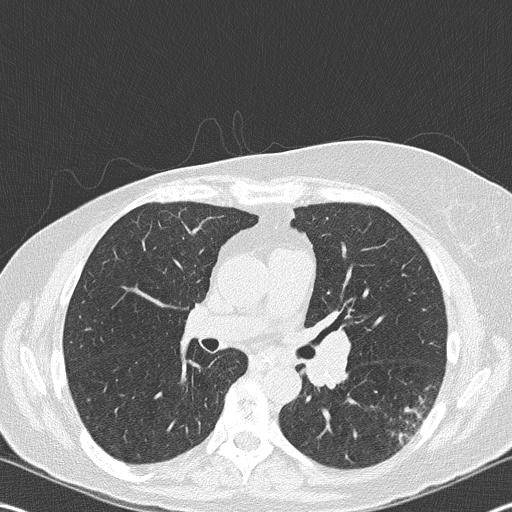
Low-dose screening chest CT, one axial slice; slice 103 of 177 in the series (ordered by position); 120 kVp; lung window (W 1500 / L -600 HU); 2 mm slice thickness; 512 × 512 image matrix, field of view 342 × 342 mm.
Annotated regions visible in this slice (manually delineated by an expert):
- lesion 1 (tumor): box from (x=399, y=408) to (x=421, y=441) px
- lesion 2 (nodule, hilum of left lung): (x=309, y=340)–(x=346, y=382)